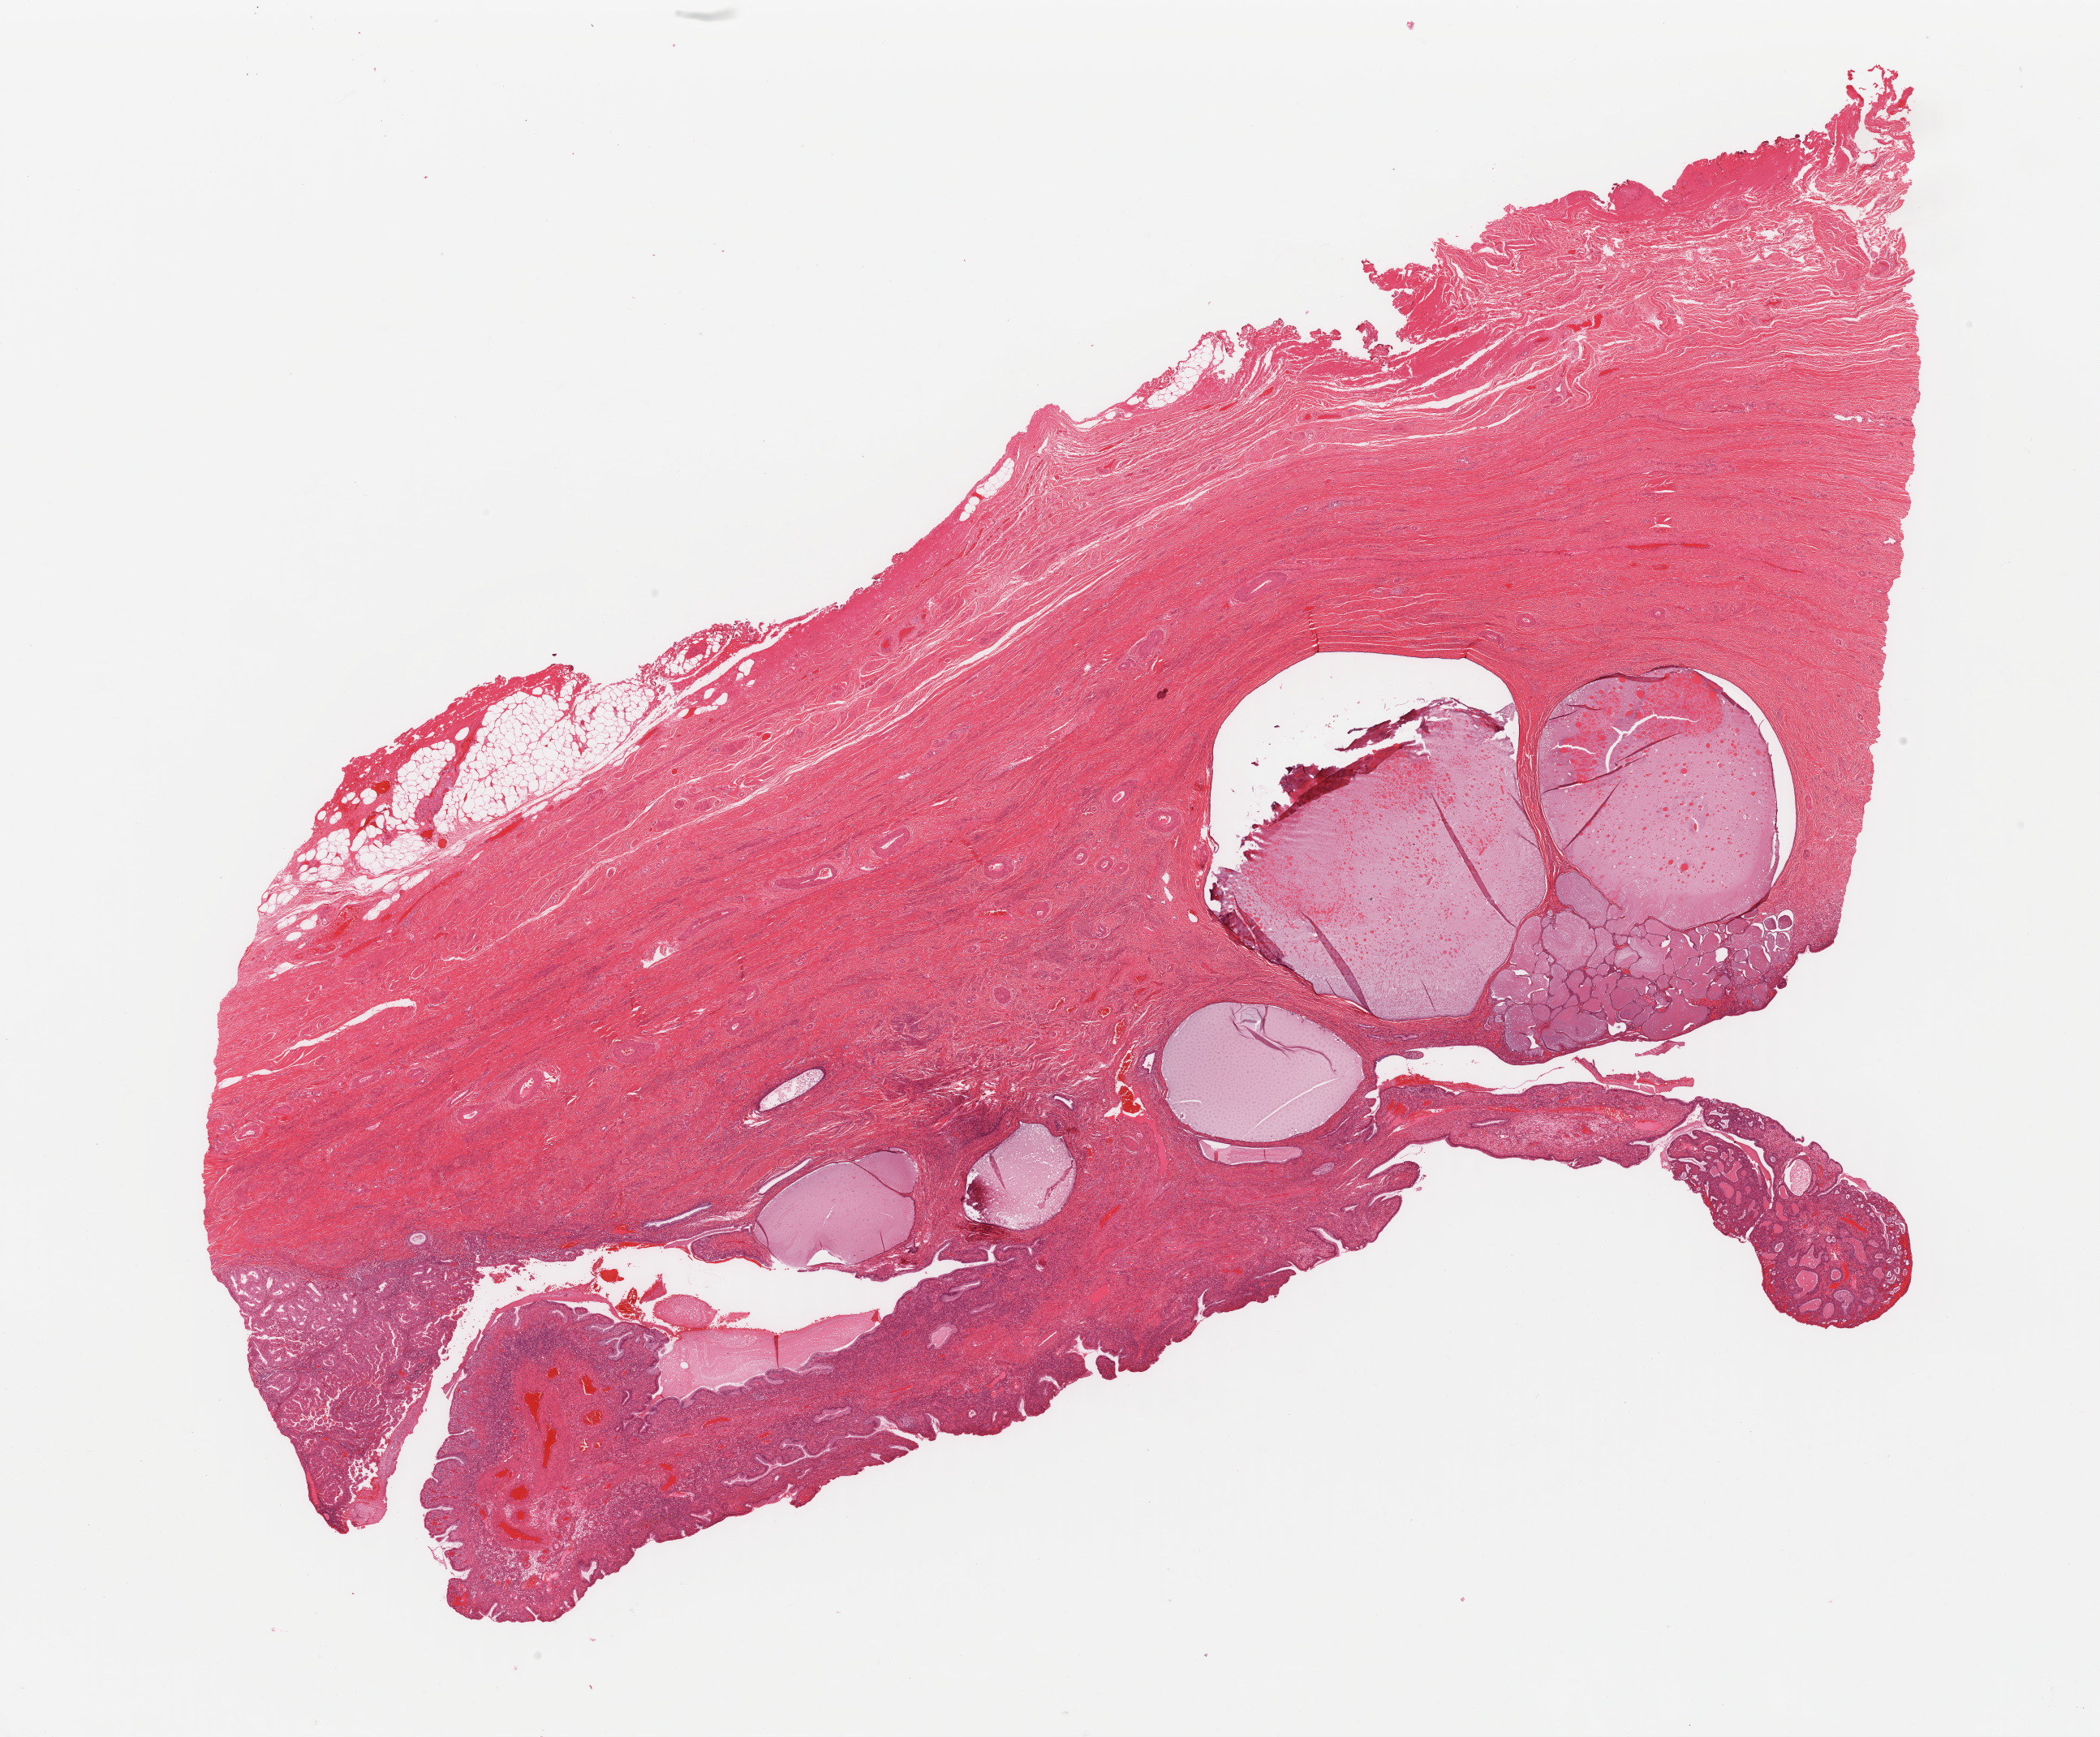
Digitized Hematoxylin and eosin (H&E) stained tissue section (whole slide) — shown as a low-resolution overview of the whole scanned area (about 20.4 x 16.9 mm), formalin-fixed paraffin-embedded (FFPE) diagnostic section, uterus, primary tumour sample. Patient: female, age at initial diagnosis 60 years. Histologic grade: G1 (well differentiated).
Diagnosis: Endometrioid adenocarcinoma, NOS (endometrium). FIGO stage: IIB.